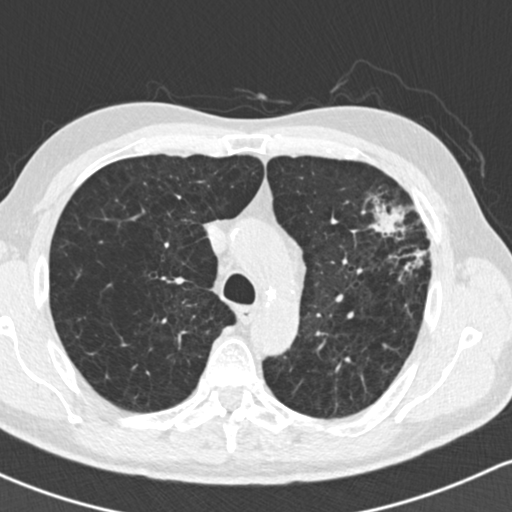
Chest CT (low-dose screening protocol), one axial image; first (baseline) screen; lung window (W 1500 / L -600 HU); standard (soft-tissue) reconstruction kernel (B30f); 120 kVp; slice 51 of 162 in the series. Male participant, aged 61 years at enrolment. Former smoker at enrolment.
Expert reader's lesion annotation, bounding box <352,184,444,288> (left, top, right, bottom; pixels). Reader record for this screening exam (exam-level; its link to the box is not recorded): non-calcified nodule or mass ≥4 mm, left upper lobe, 35 × 35 mm, spiculated (stellate) margins, soft tissue attenuation. Official screen result: positive, change unspecified: nodule(s) >= 4 mm or enlarging nodule(s), mass(es), or other non-specific abnormalities suspicious for lung cancer.